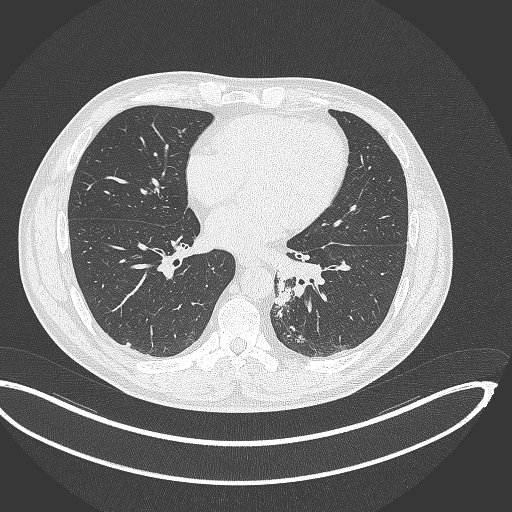
Chest CT, one axial slice. Position 145 of 362 along the scan axis. Lung window (W 1500 / L -600 HU). 1 mm slice thickness. 512 × 512 image matrix, field of view 442 × 442 mm. Patient: male, 50 years. Case-level facts recorded for this patient, not image findings: clinical TNM (as recorded): T2a N3 M0.
Structures marked on this image (bounding box drawn by a radiologist):
- lung tumour (recorded histology: squamous cell carcinoma): bounding box <271,279,295,308> (left, top, right, bottom; pixels)